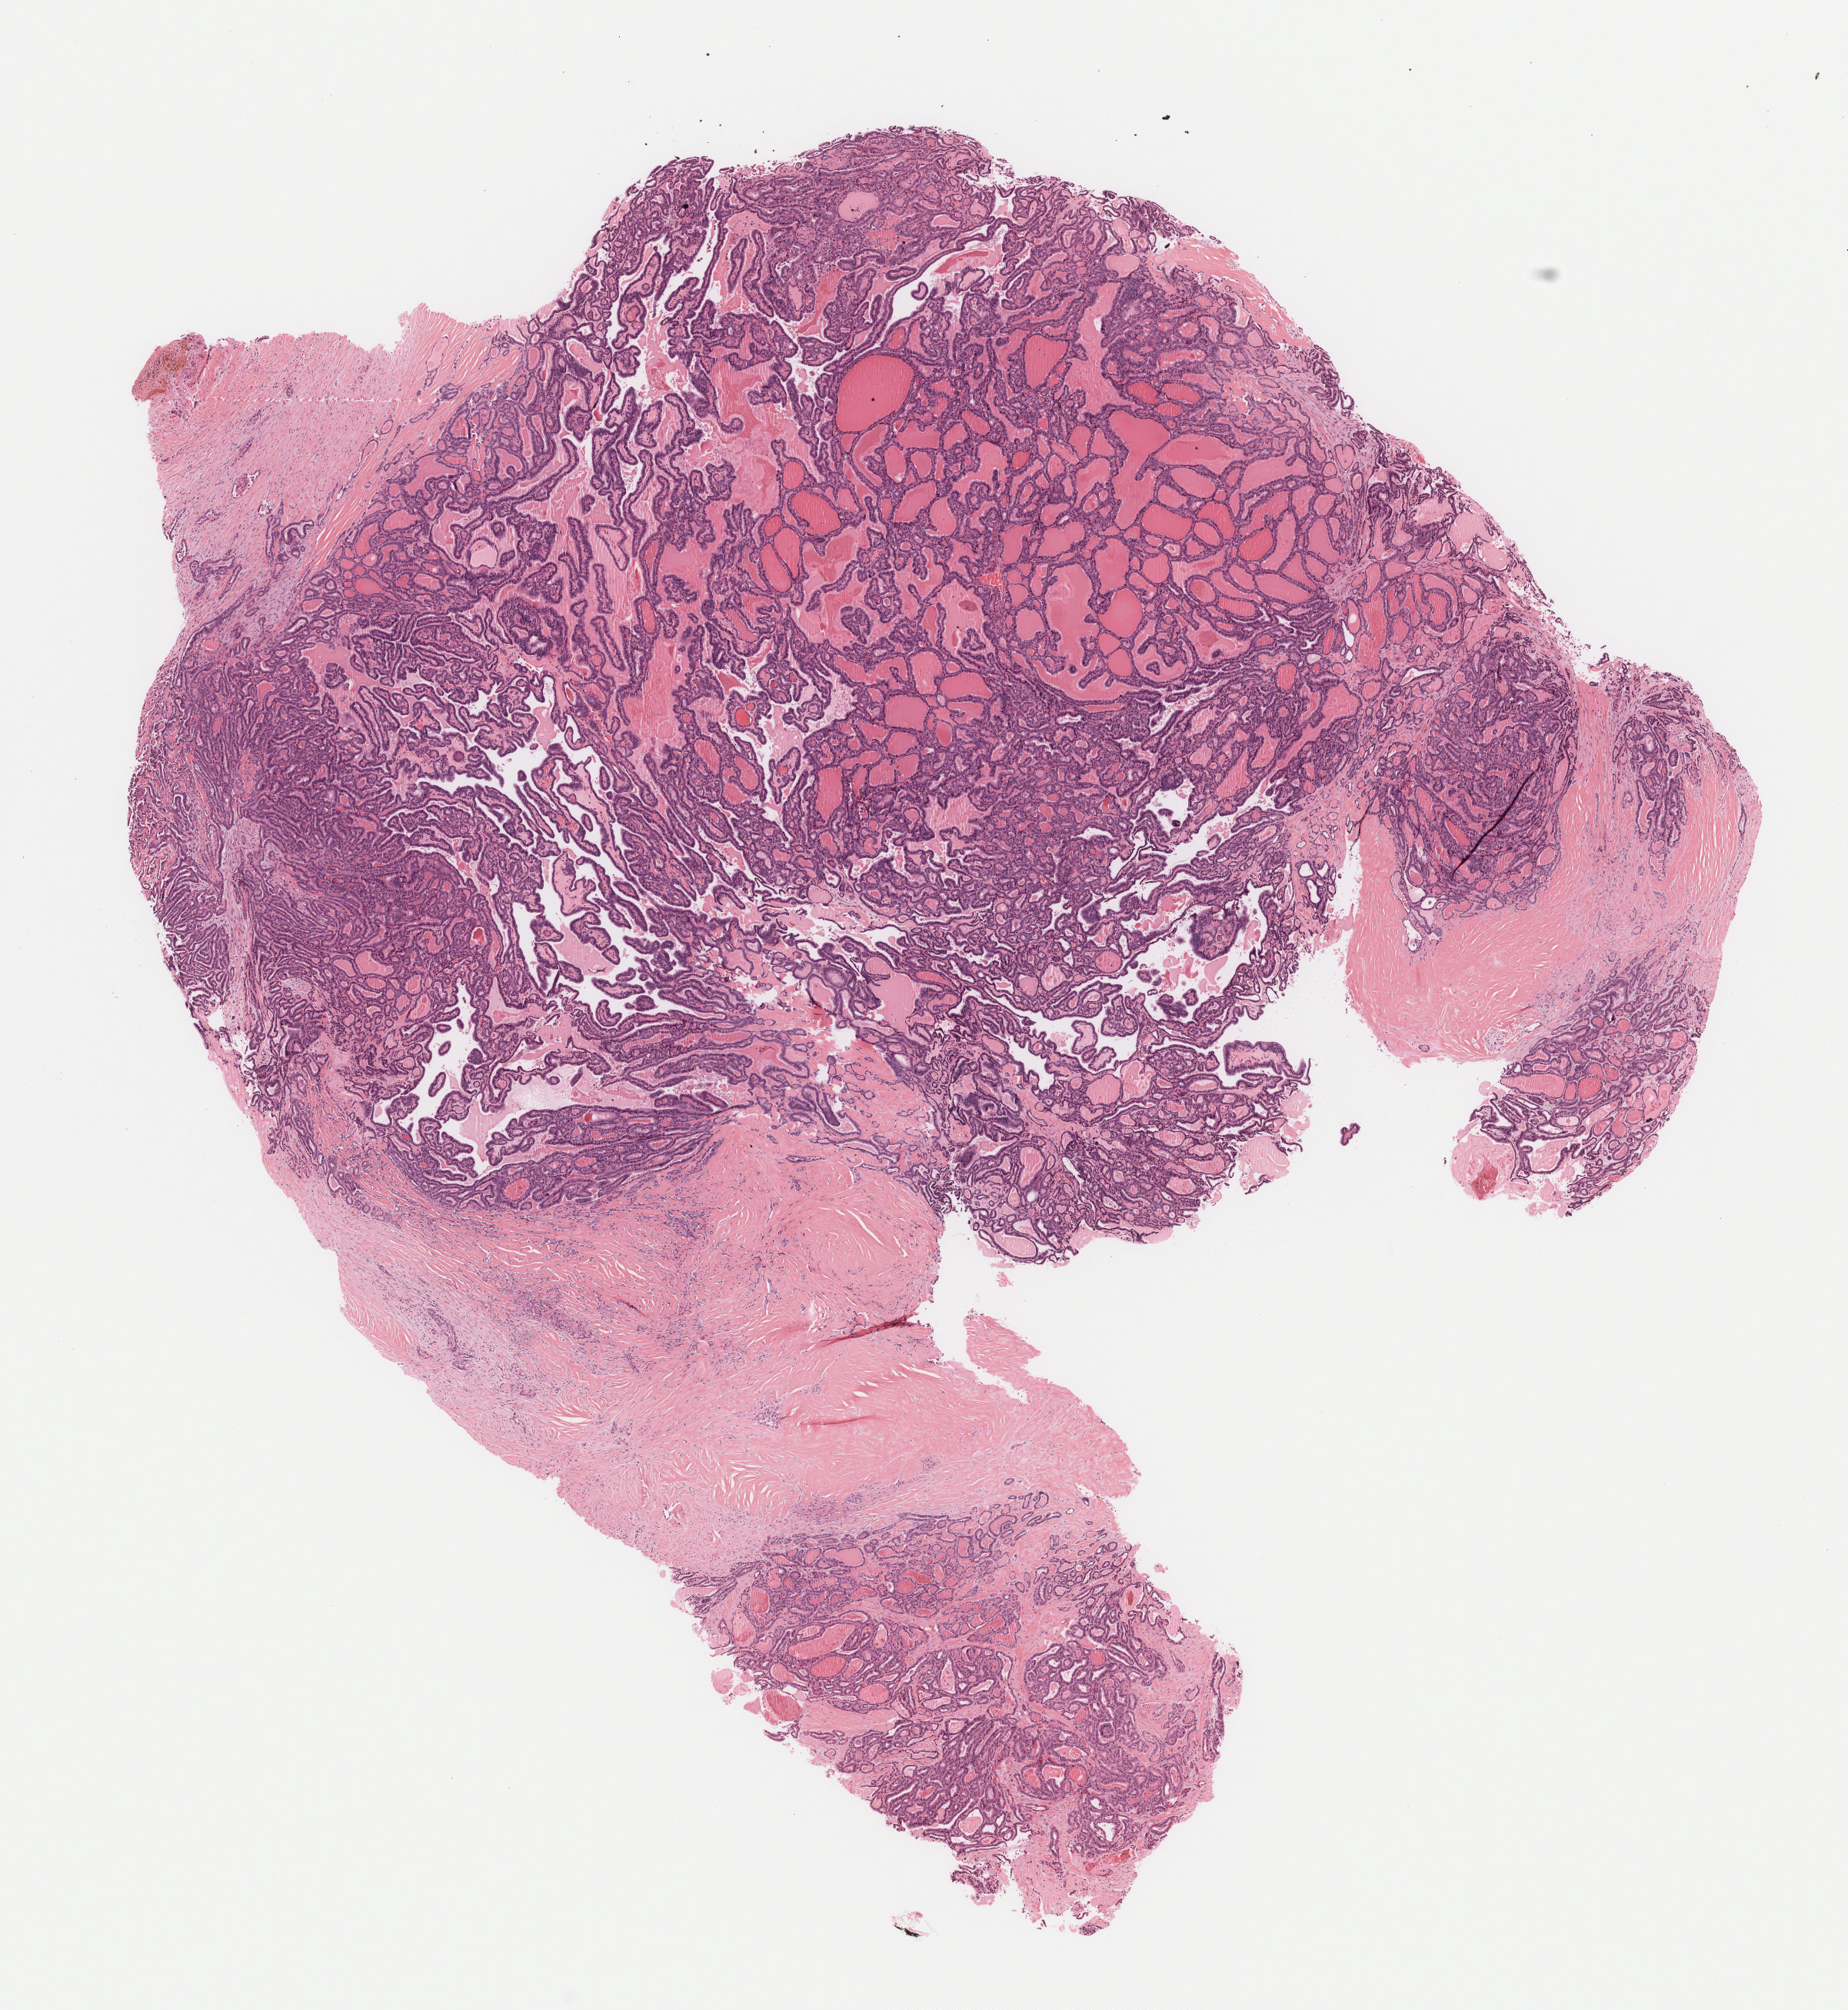
Digitized H&E-stained tissue section (whole slide), a low-resolution overview of the entire scanned area, about 9.7 x 10.5 mm. Formalin-fixed paraffin-embedded (FFPE) diagnostic section. Thyroid, primary tumour sample. Female, age 47 years at initial diagnosis.
AJCC pathologic stage: I (7th edition). Histologic diagnosis: Papillary adenocarcinoma, NOS (thyroid gland).